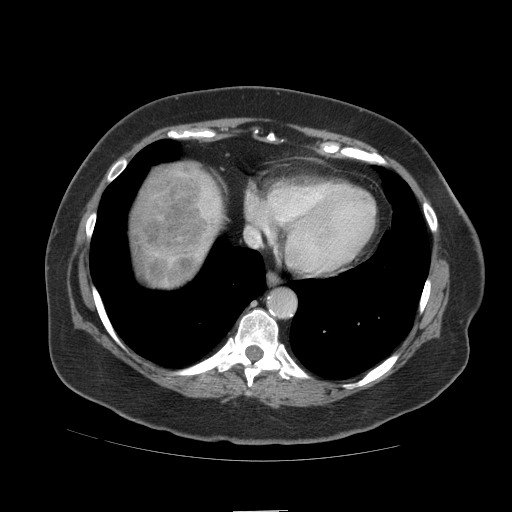
Contrast-enhanced abdominal CT (liver protocol), one axial slice; reconstruction kernel STANDARD; soft-tissue window (W 400 / L 40 HU); 2.5 mm slice thickness; 512 × 512 image matrix. From the clinical record (not read from this slice): diagnosis: hepatocellular carcinoma (patient treated with transarterial chemoembolisation; whether this scan precedes or follows treatment is not stated here); TNM stage (as recorded): Stage-IVB; Child-Pugh class: A; tumour differentiation: poorly differentiated; tumour nodularity: multinodular.
Annotated regions visible in this slice (semi-automatic segmentation, software-assisted and operator-edited):
- liver parenchyma outside the tumour (the mass and vessels are separate outlines, so this box may not span the whole liver): bounding box [x1, y1, x2, y2] px = [140, 164, 222, 286]
- mass: [130, 167, 221, 283]